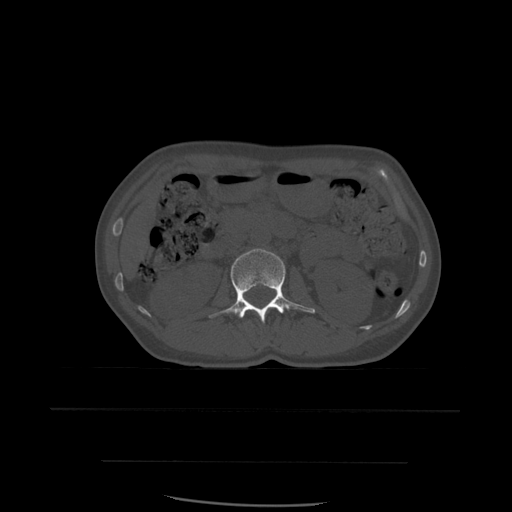
CT including the spine, one axial slice. Position 226 of 574 along the scan axis. Bone window (W 1800 / L 400 HU). 1.25 mm slice thickness. 512 × 512 image matrix, field of view 392 × 392 mm. Patient age 48 years. Case-level facts recorded for this patient, not image findings: primary cancer: lung; vertebrae with lytic lesions (as recorded): T11.
Structures marked on this image (semi-automatically segmented with operator editing):
- L2 vertebra: bounding box (x1, y1, x2, y2) in pixels: (209, 249, 316, 323)